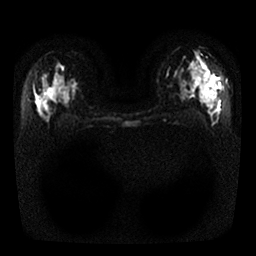
Breast MRI, one axial slice. Diffusion-weighted series; image 2 of 4 stored at this slice position (different b-values; order by instance number). 1.5 T. 4 mm slice thickness. 256 × 256 image matrix, field of view 320 × 320 mm. Female patient.
Outlined on this slice (manually delineated by an expert):
- tumour on diffusion-weighted imaging: bounding box (x1, y1, x2, y2) in pixels: (202, 68, 220, 89)